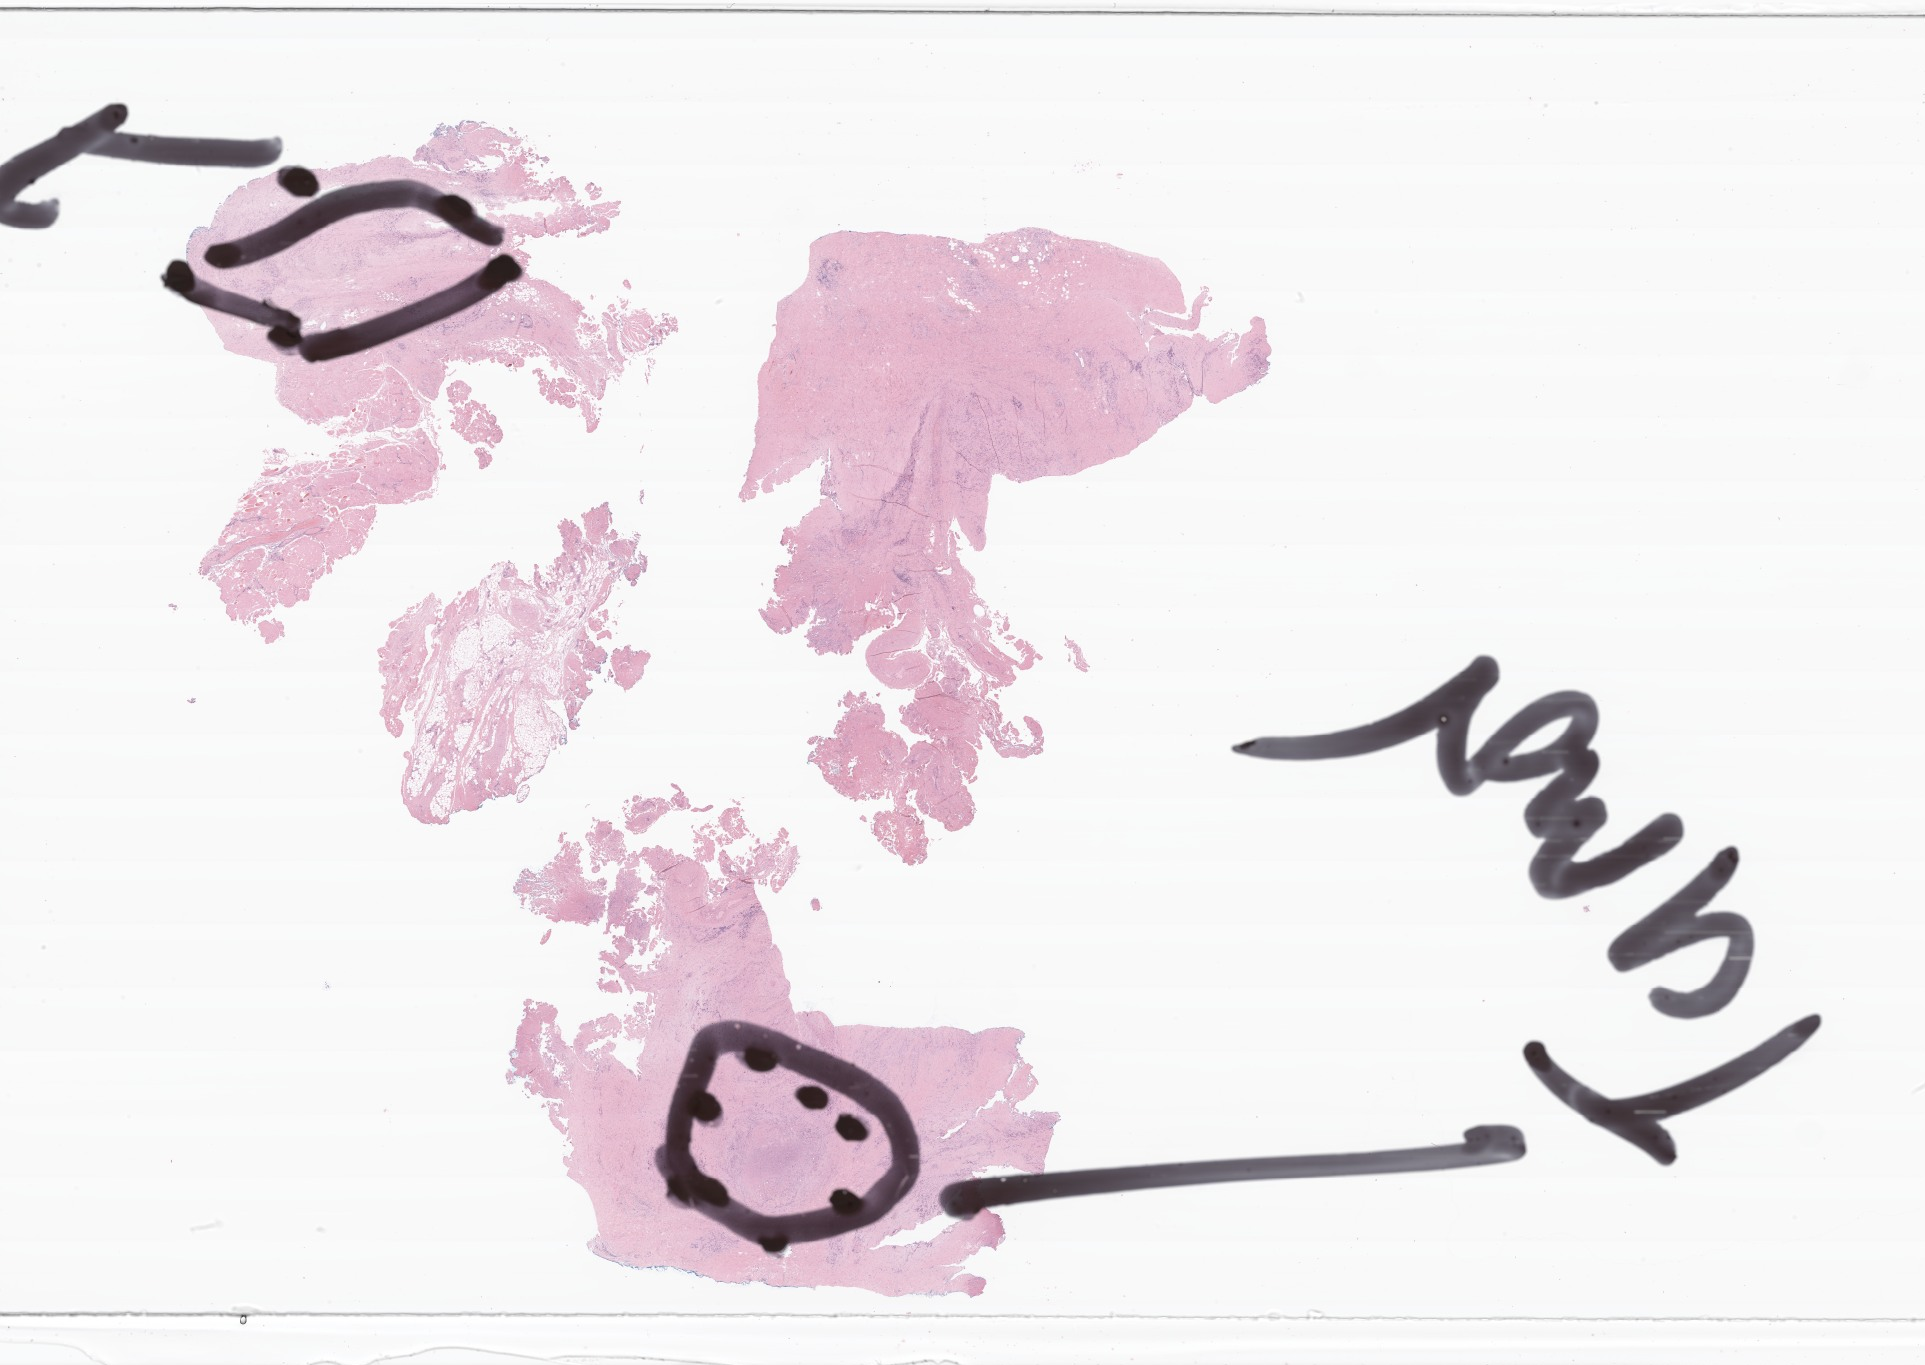
Whole-slide image, hematoxylin and eosin (H&E) stain of tumor tissue from the thyroid — low-resolution overview of the scanned area, about 32.4 x 23.0 mm; FFPE section. Patient female; age 162 months (13 years 6 months).
Diagnosis (ICD-O-3 morphology term): Medullary carcinoma, NOS.